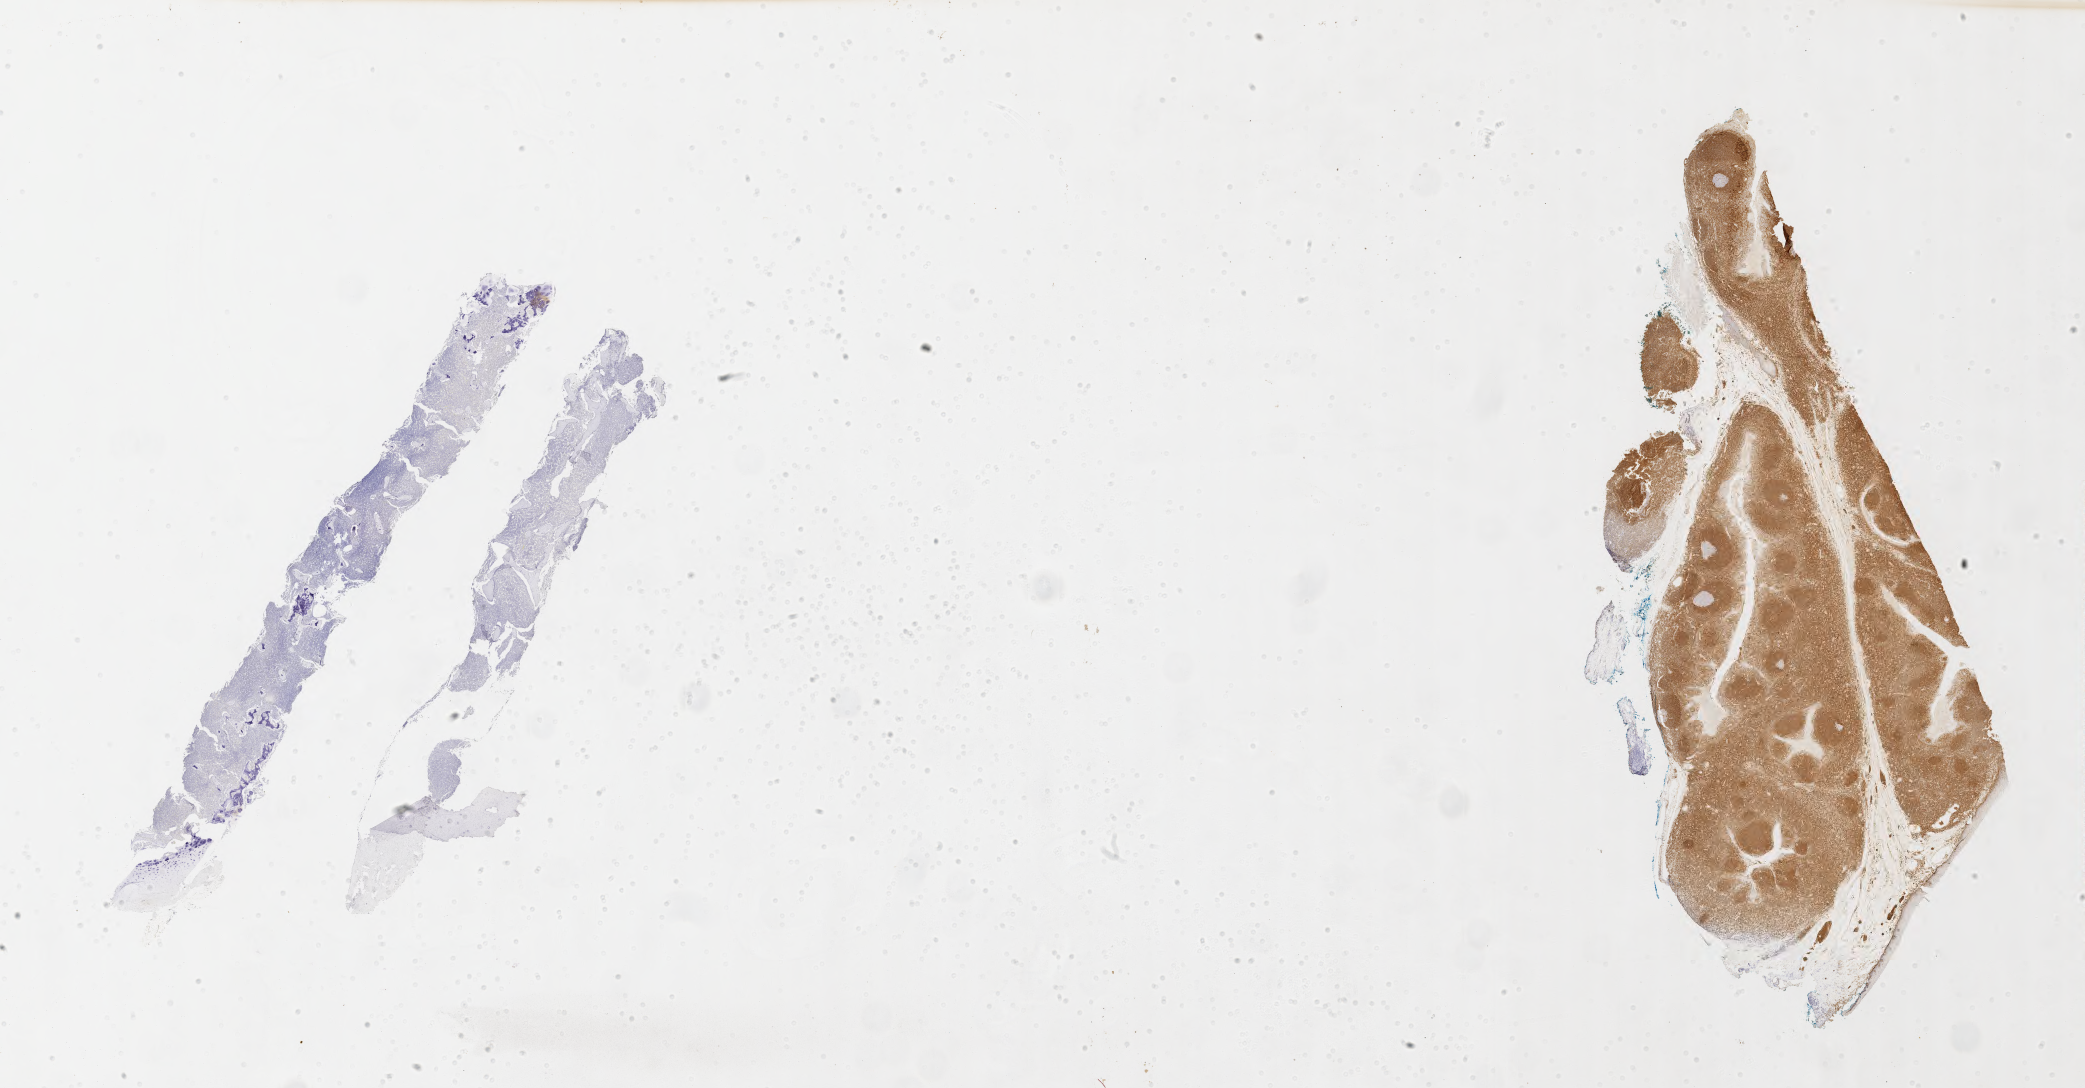
IHC for BCL2, whole-slide image, low-resolution overview of the scanned area, about 33.7 x 17.6 mm. Tumor tissue. Anatomic site: bone marrow. Patient: male, 16 years old.
- histologic diagnosis: Burkitt lymphoma, NOS